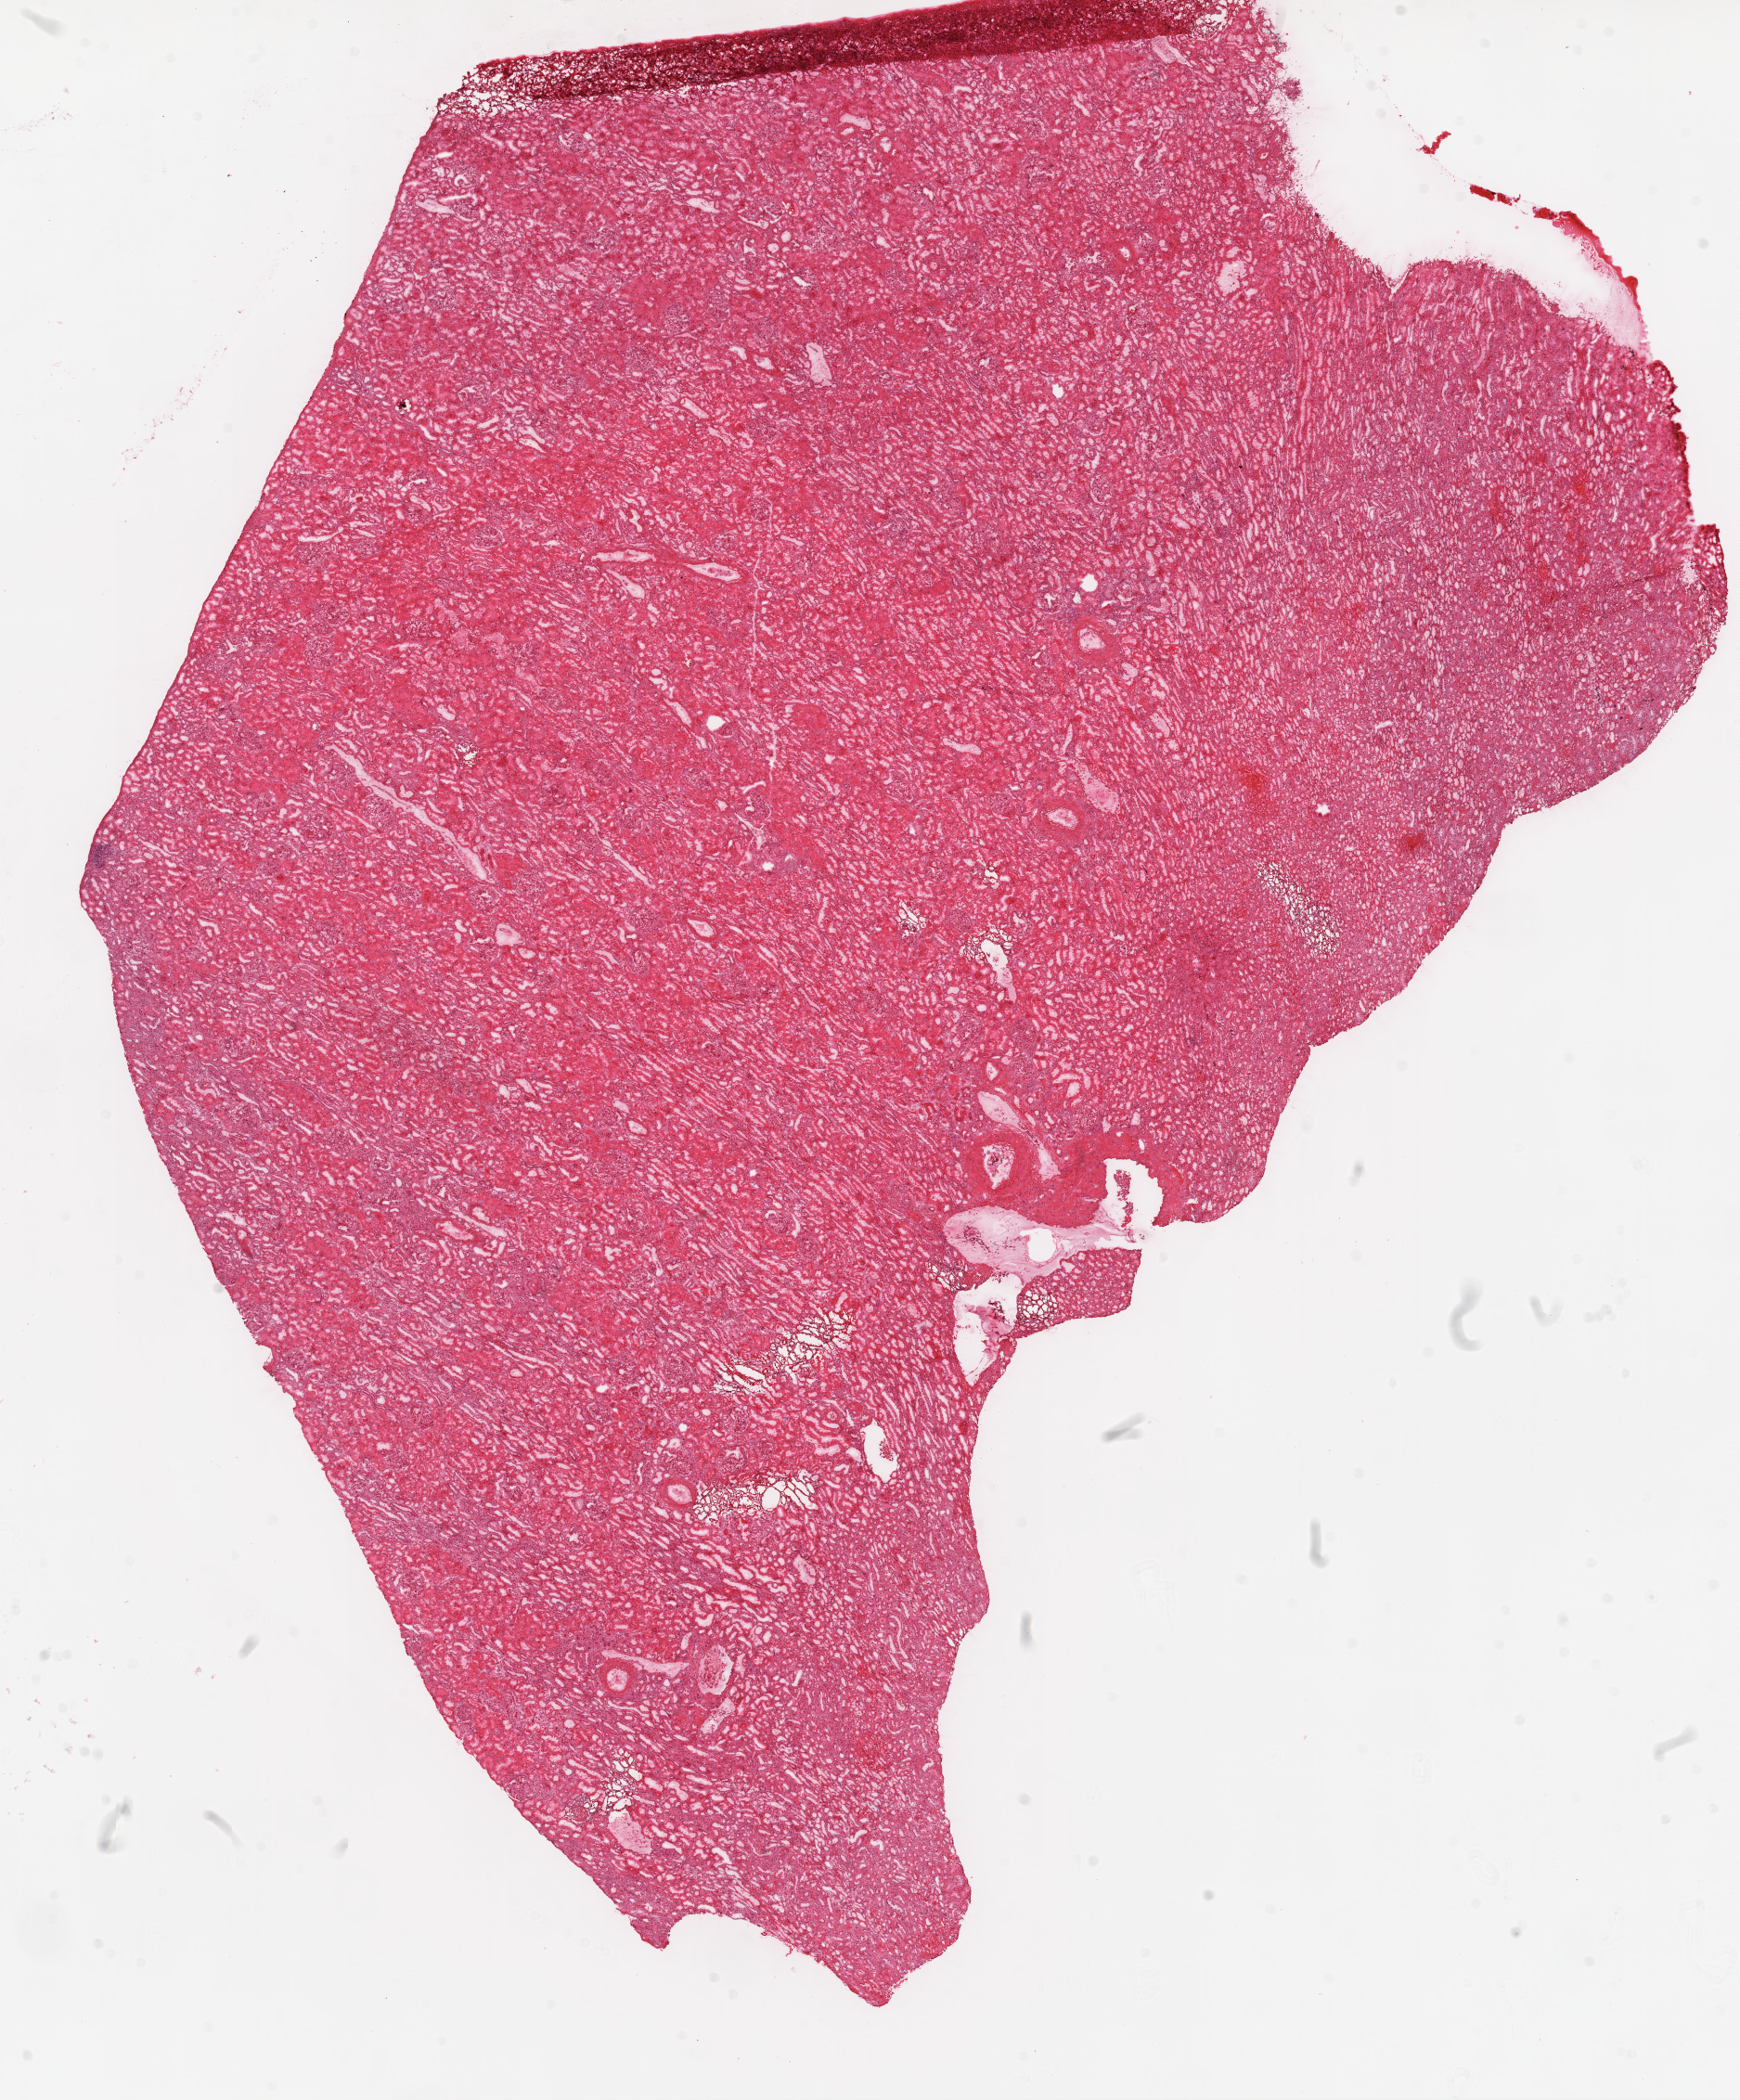
Digitized H&E-stained tissue section (whole slide), a low-resolution overview of the entire scanned area, about 15.0 x 18.2 mm, frozen section from the top of the tissue portion, sample: solid tissue normal (non-tumour tissue), kidney. Female patient; age at initial diagnosis 53 years.
This section: solid tissue normal sample (biorepository sample class). Patient diagnosis: Clear cell adenocarcinoma, NOS.